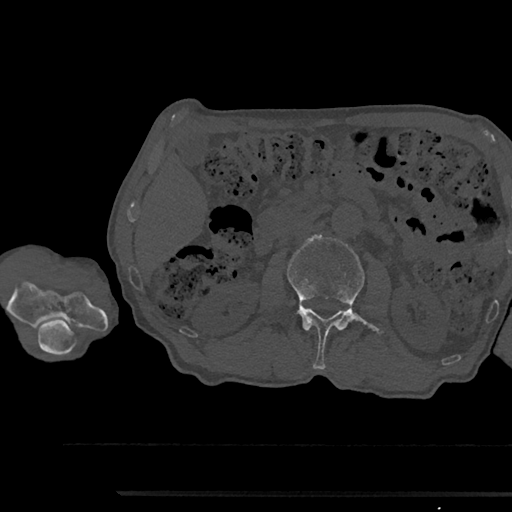
CT including the spine, one axial slice; position 561 of 797 along the scan axis; bone window (W 1800 / L 400 HU); 0.5 mm slice thickness; 512 × 512 image matrix, field of view 367 × 367 mm. Patient: male, 79 years. From the clinical record (not read from this slice): primary cancer: prostate.
Outlined on this slice (semi-automatic segmentation, software-assisted and operator-edited):
- L2 vertebra: box from (x=287, y=235) to (x=380, y=369) px